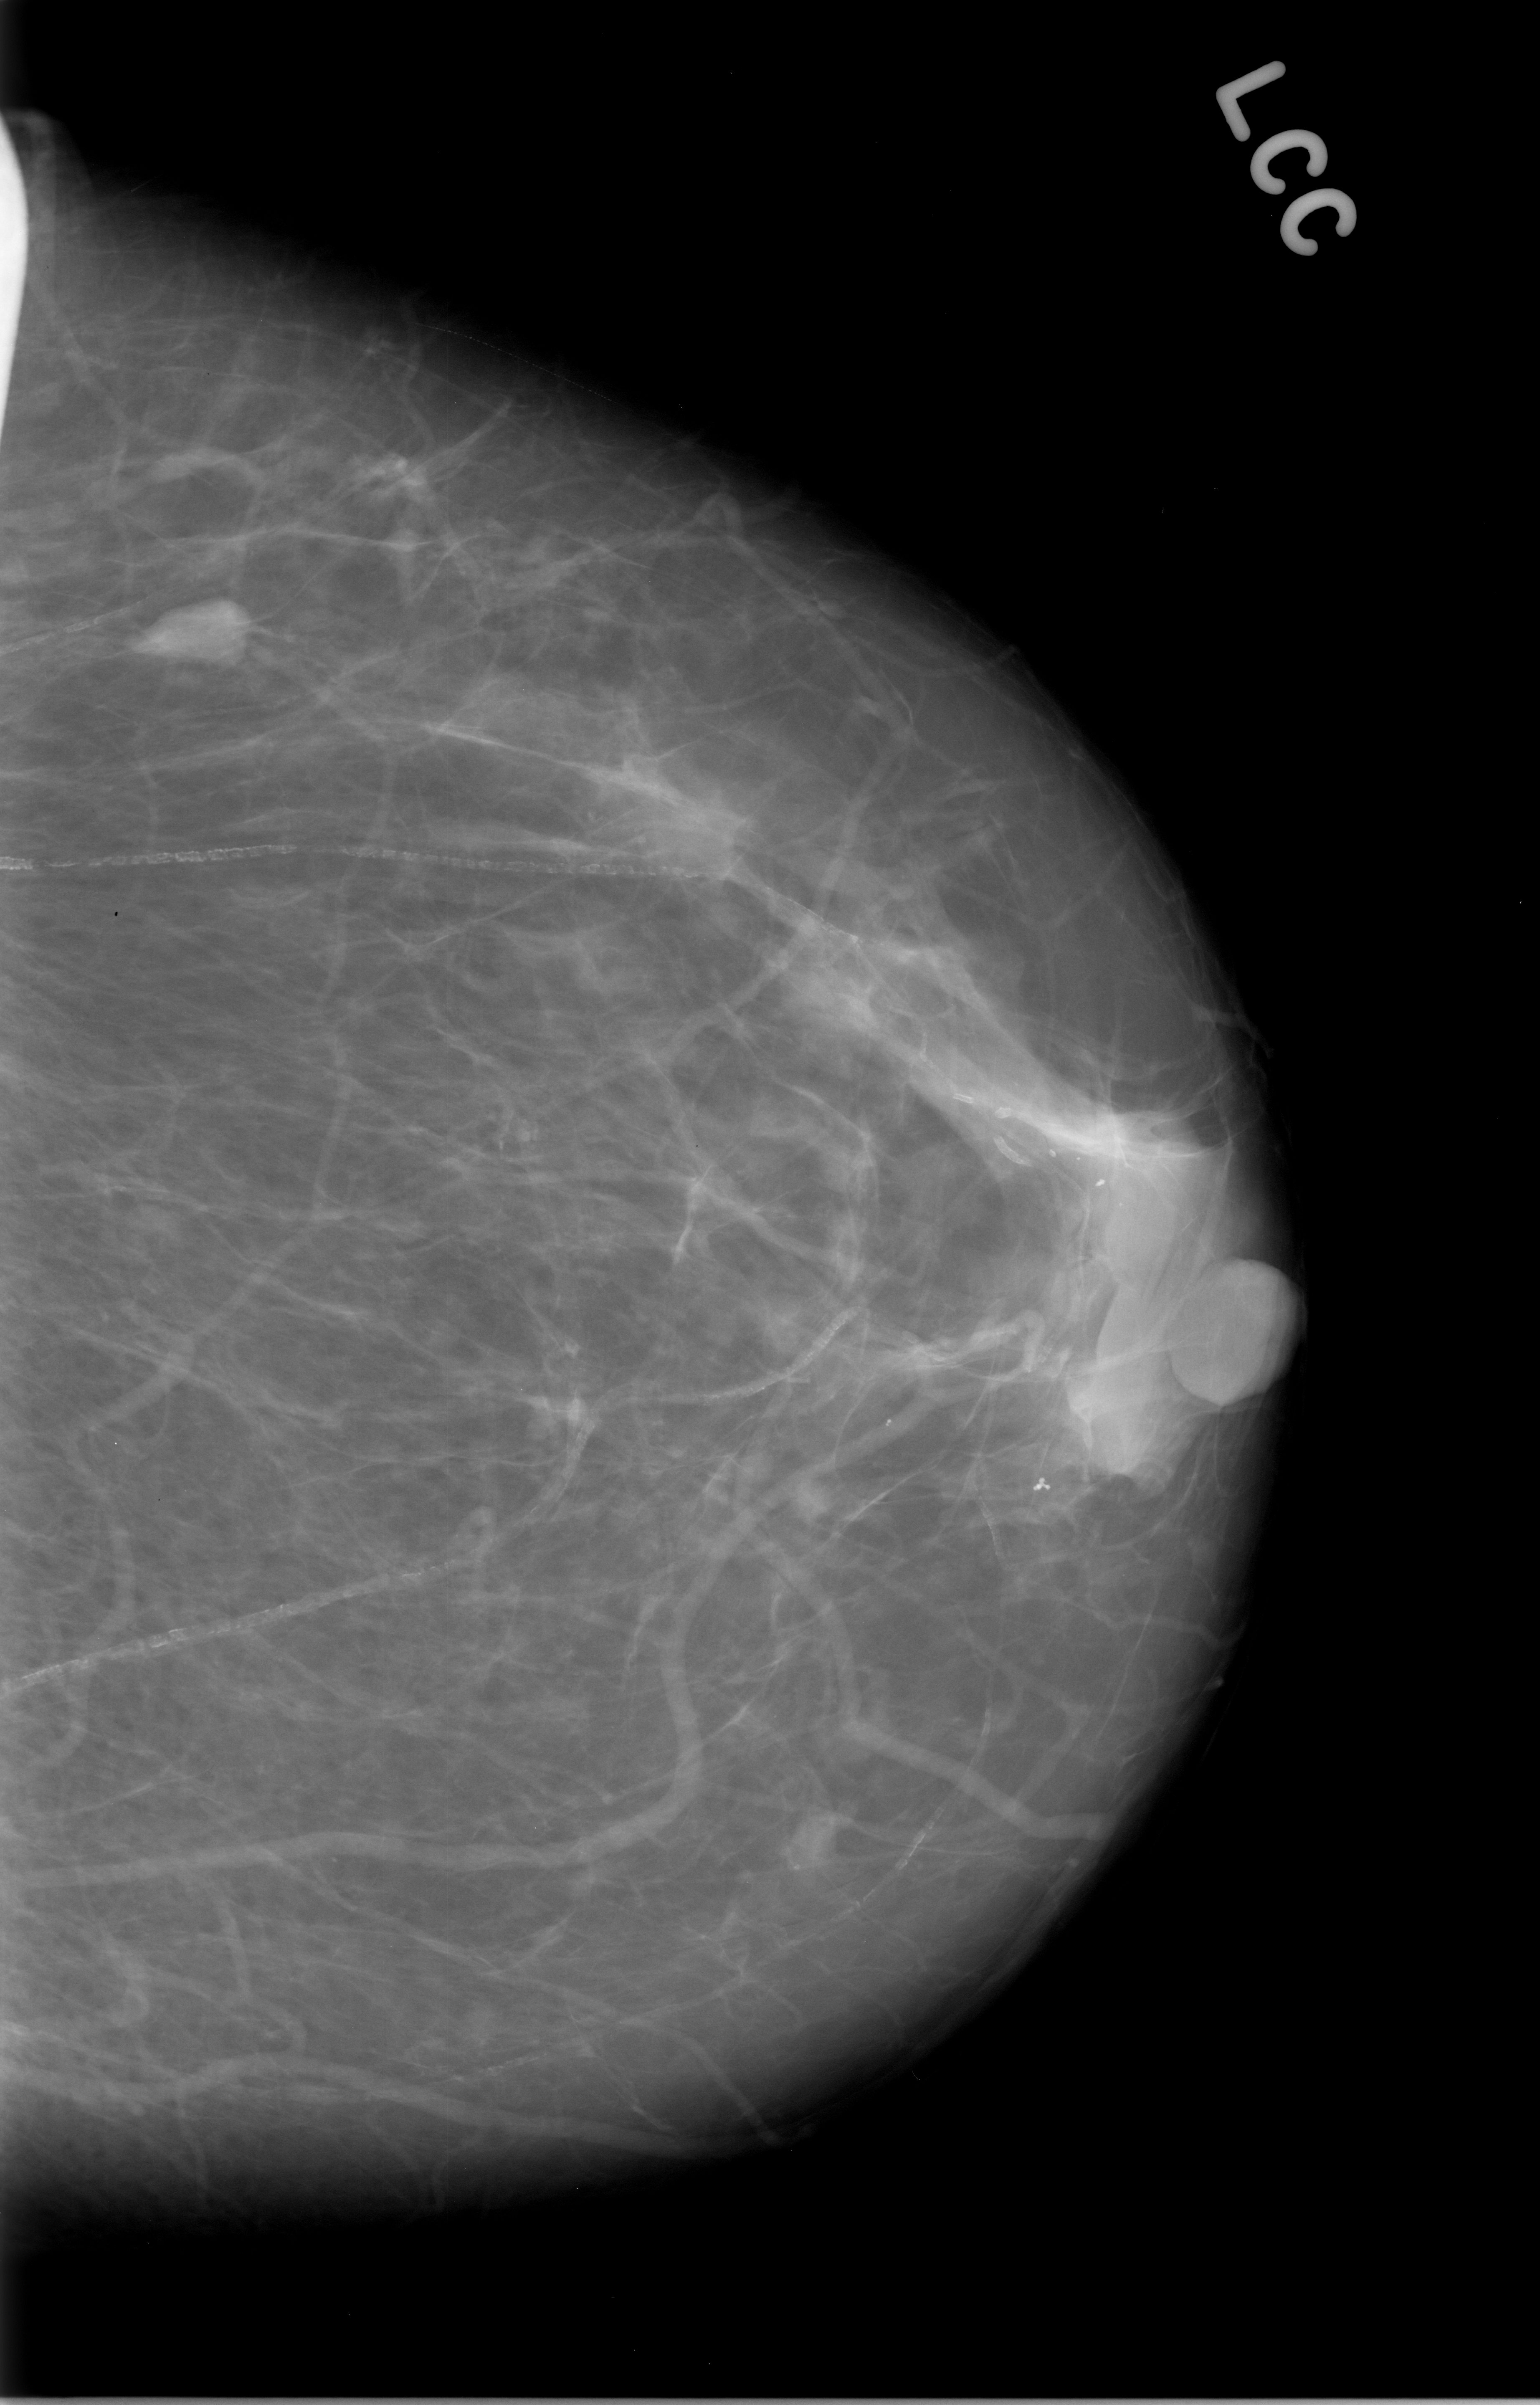
Digitized screen-film mammogram, left breast, craniocaudal (CC) view, BI-RADS breast density category 1 (scale 1–4).
Finding: mass, shape oval, margins circumscribed; BI-RADS assessment category 2; subtlety rating 5 on a 1 (subtle) to 5 (obvious) scale; pathology (as recorded): benign.